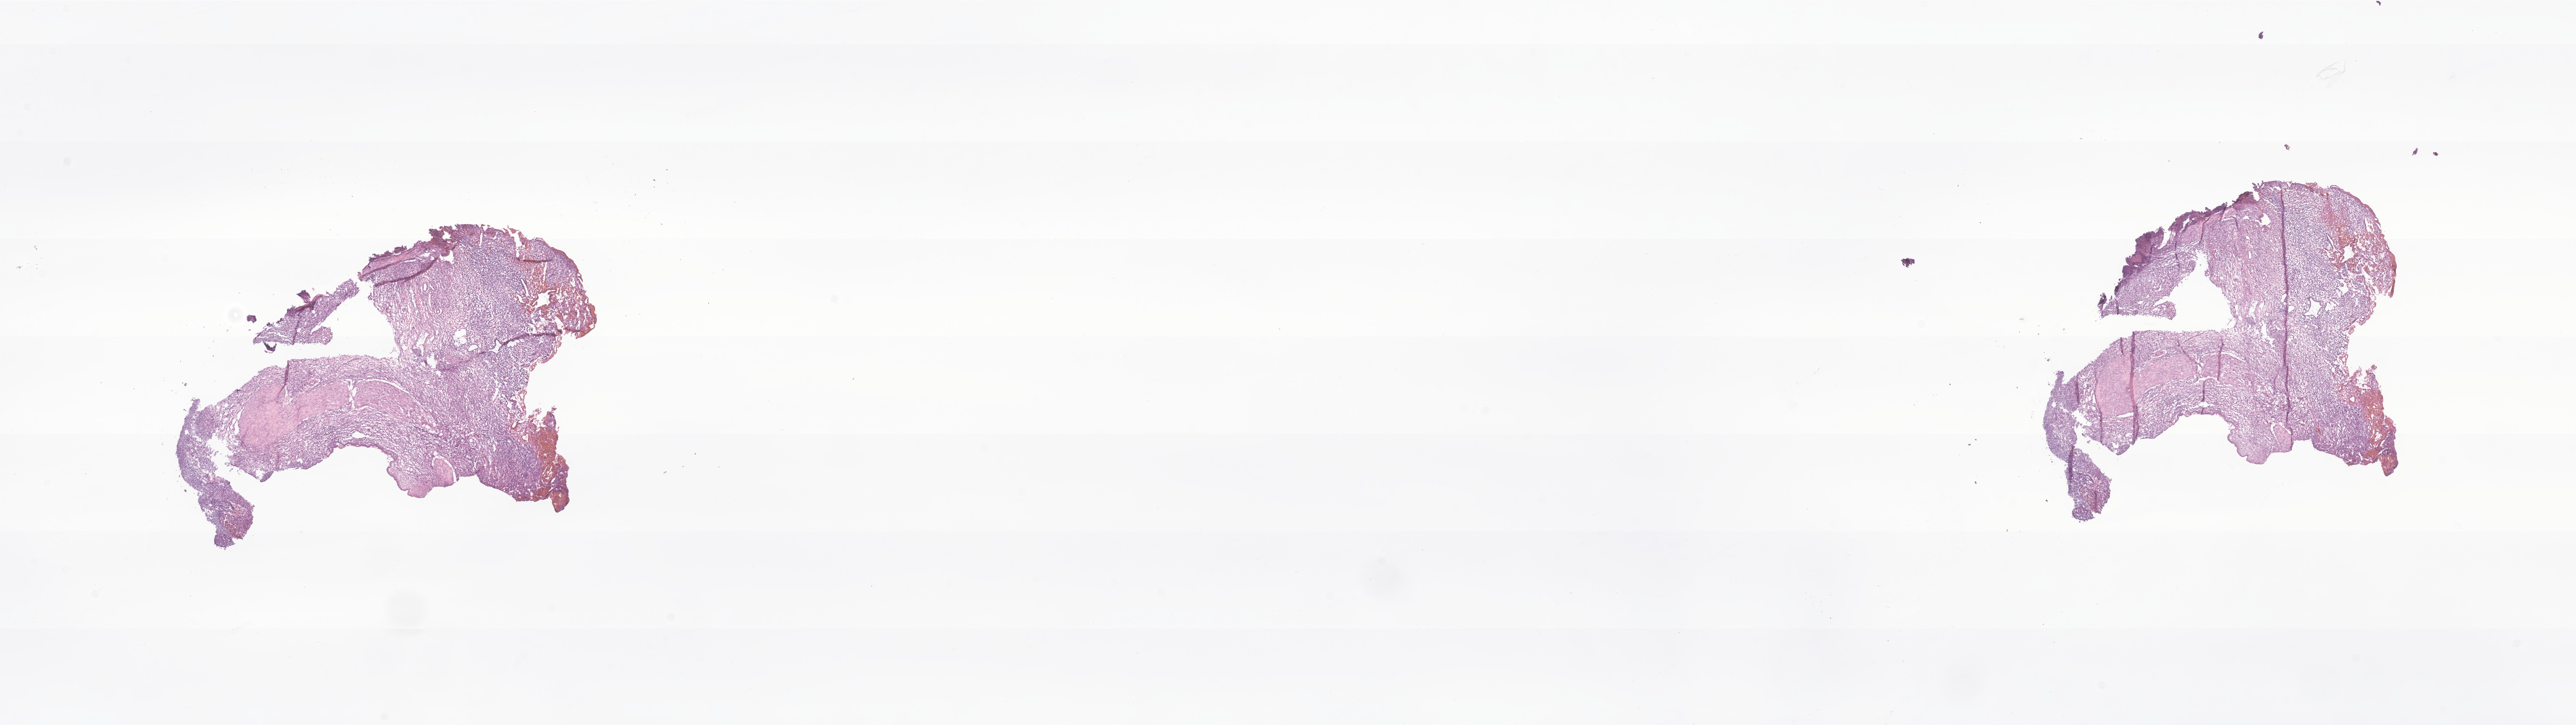
Whole-slide image, hematoxylin and eosin (H&E) stain of tumor tissue from the spinal cord, low-resolution overview of the scanned area, about 28.2 x 7.9 mm; frozen section. Patient male; age 490 days (about 1.3 years).
- diagnosis (ICD-O-3 morphology term): Pleuropulmonary blastoma